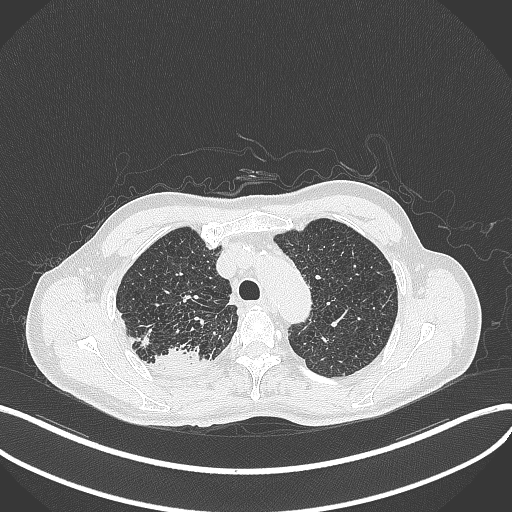
Chest CT, one axial slice. Position 346 of 428 along the scan axis. Lung window (W 1500 / L -600 HU). 1 mm slice thickness. 512 × 512 image matrix, field of view 400 × 400 mm. Patient: male, 79 years. Case-level facts recorded for this patient, not image findings: clinical TNM (as recorded): T3 N0 M0.
Annotated regions visible in this slice (rectangle marked by the reading radiologist):
- lung tumour (recorded histology: adenocarcinoma): box from (x=152, y=343) to (x=212, y=378) px